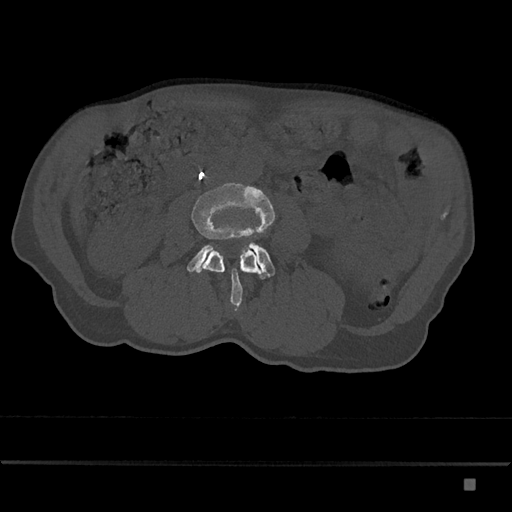
CT including the spine, one axial slice. Position 379 of 797 along the scan axis. 120 kVp. Bone window (W 1800 / L 400 HU). 0.5 mm slice thickness. 512 × 512 image matrix, field of view 390 × 390 mm. Patient: male, 72 years. From the clinical record (not read from this slice): primary cancer: prostate.
Annotated regions visible in this slice (semi-automatically segmented with operator editing):
- L3 vertebra: bounding box <191,181,275,311> (left, top, right, bottom; pixels)
- L4 vertebra: <187,242,275,280>